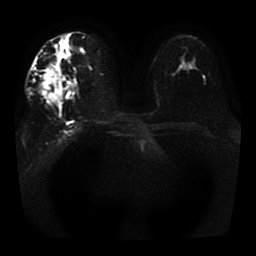
Breast MRI, one axial slice; position 23 of 41 along the scan axis; diffusion-weighted series; image 2 of 4 stored at this slice position (different b-values; order by instance number); 1.5 T; 256 × 256 image matrix, field of view 330 × 330 mm. Female patient.
Structures marked on this image (manually delineated by an expert):
- tumour on diffusion-weighted imaging: bounding box (x1, y1, x2, y2) in pixels: (40, 66, 61, 102)